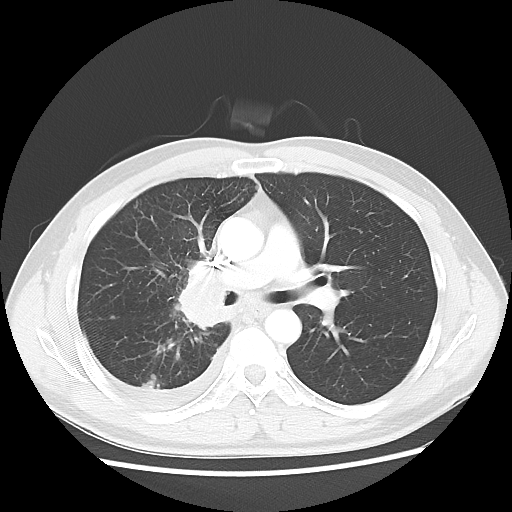
Chest CT, one axial slice. Slice 32 of 56 in the series (ordered by position). Reconstruction kernel LUNG. Lung window (W 1500 / L -600 HU). 5 mm slice thickness. 512 × 512 image matrix. Male patient, age 46 years. Case-level facts recorded for this patient, not image findings: clinical TNM (as recorded): T2 N3 M1.
Annotated regions visible in this slice (bounding box drawn by a radiologist):
- lung tumour (recorded histology: adenocarcinoma): bounding box <169,256,231,329> (left, top, right, bottom; pixels)